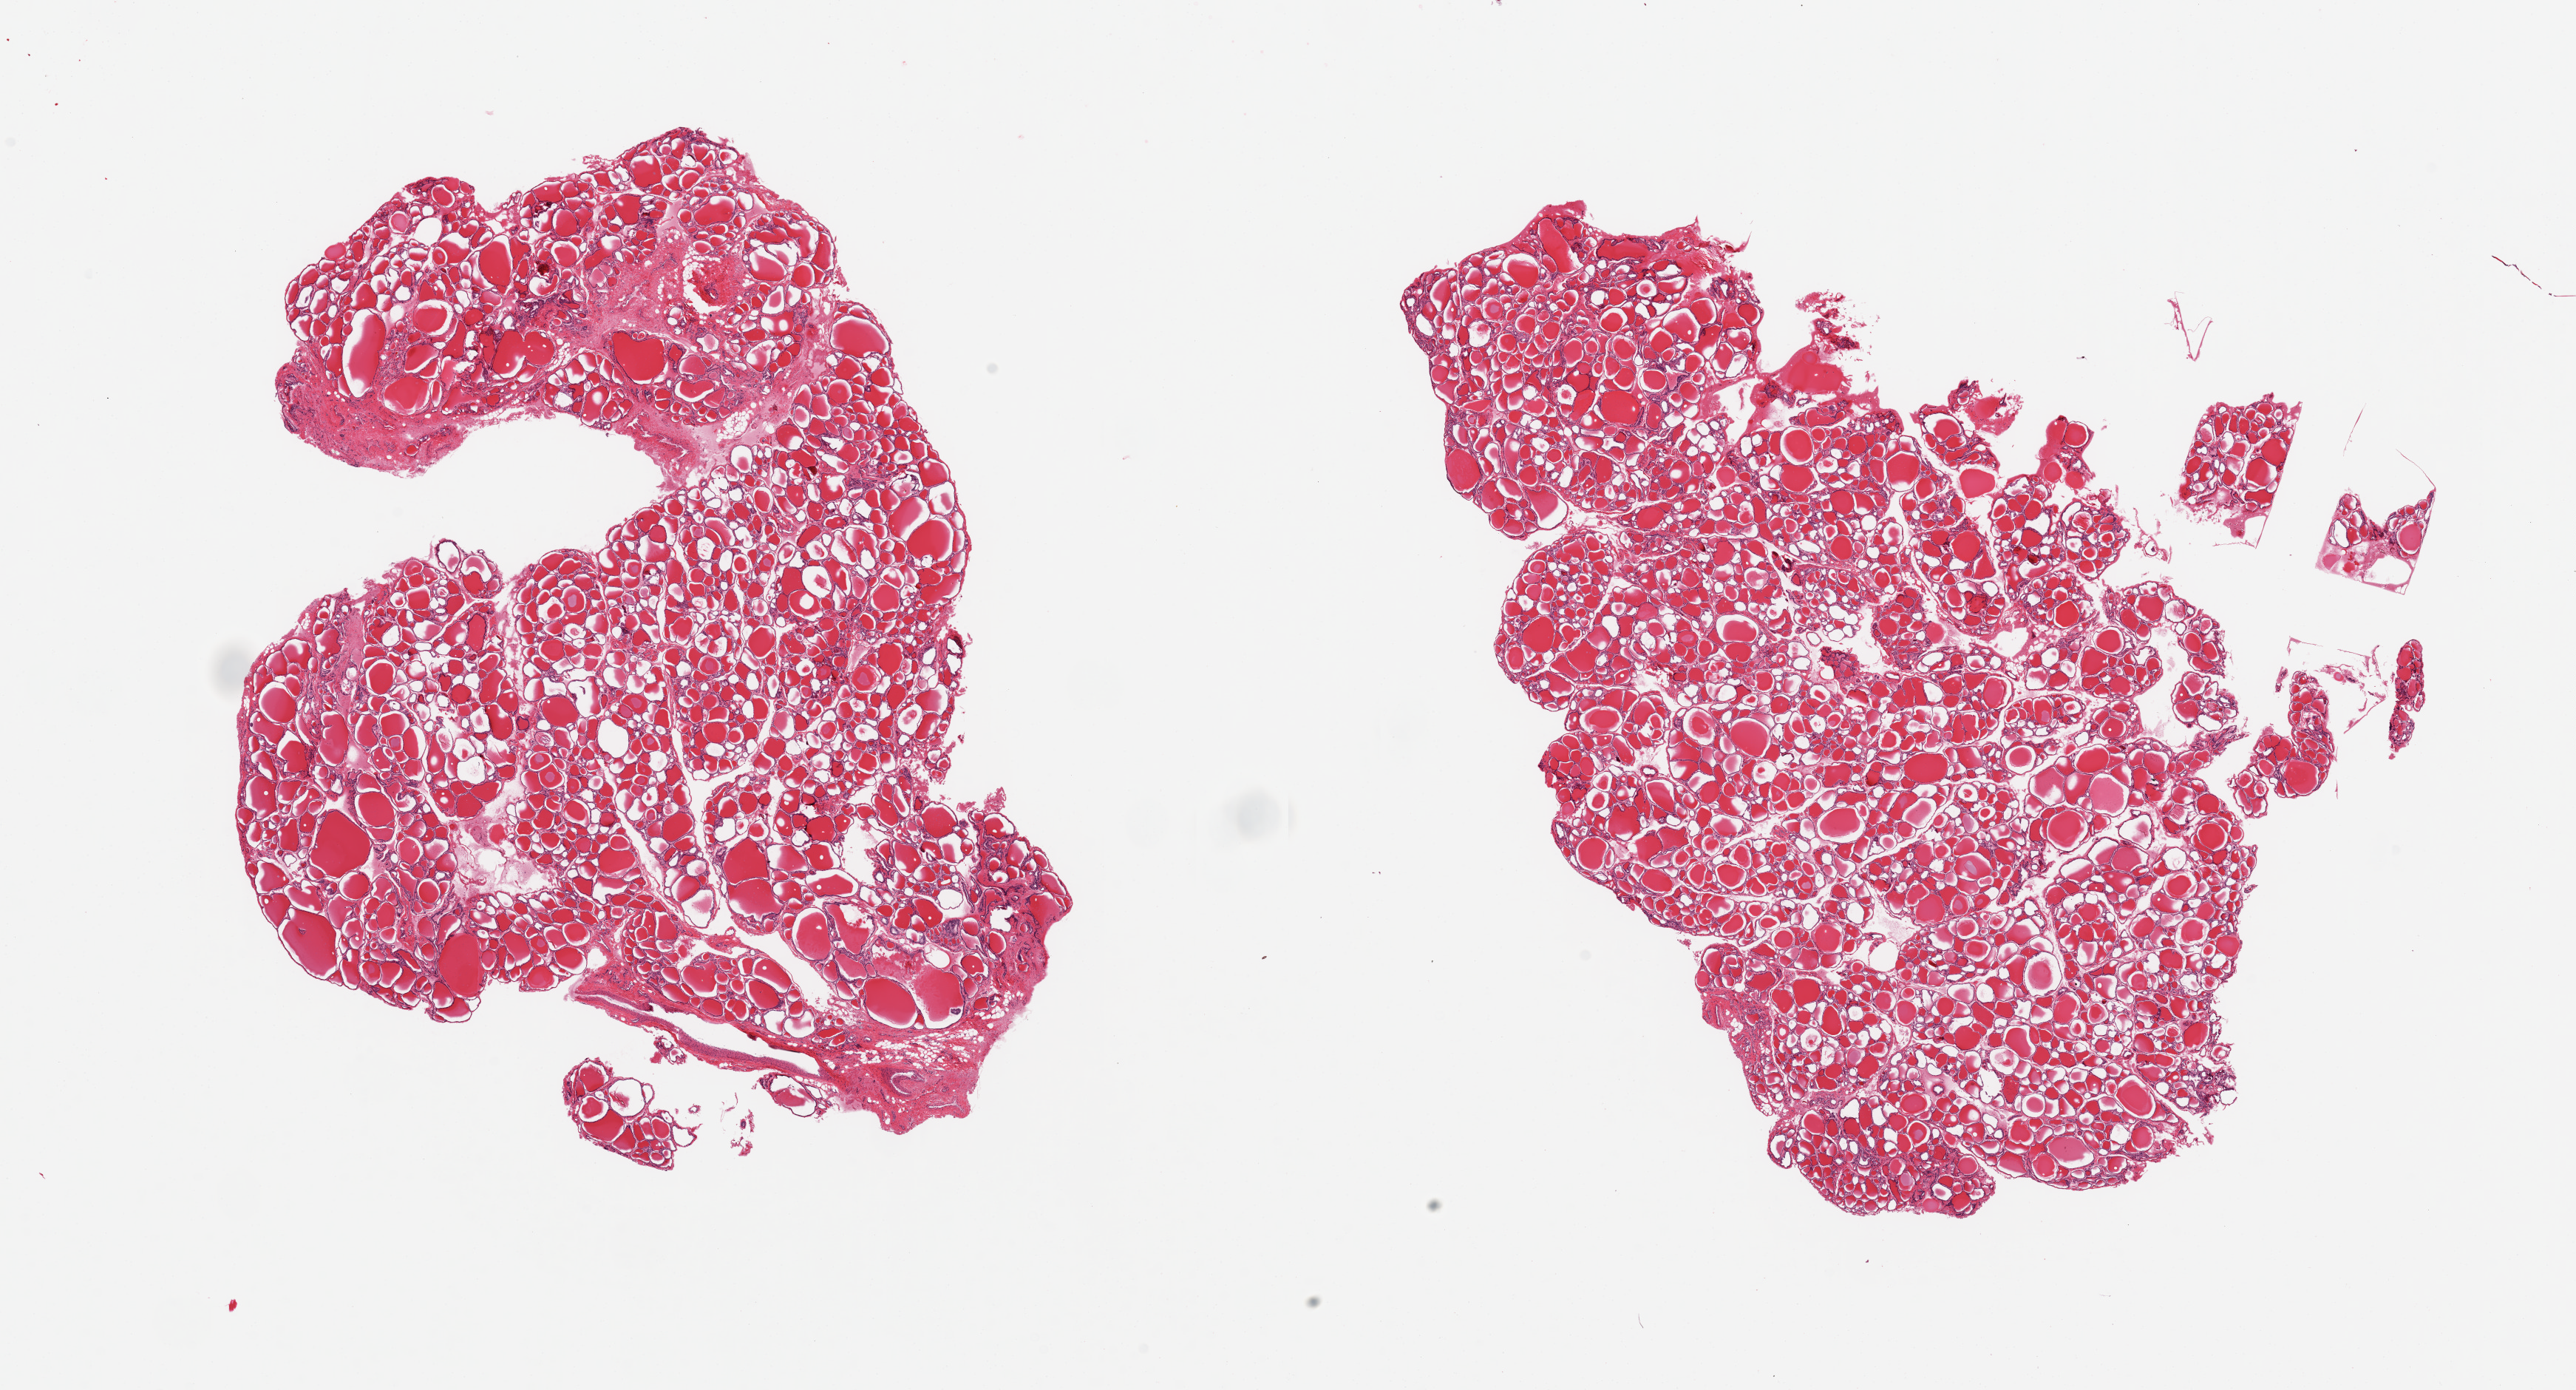
H&E whole-slide image, brightfield — shown as a low-resolution overview of the whole scanned area (about 27.6 x 14.9 mm, acquisition: 20x scan); PAXgene-fixed paraffin-embedded (PFPE) section; sampled site (target tissue): thyroid; tissue donor sample.
Review note (as recorded): 2 pieces, no abnormalities.